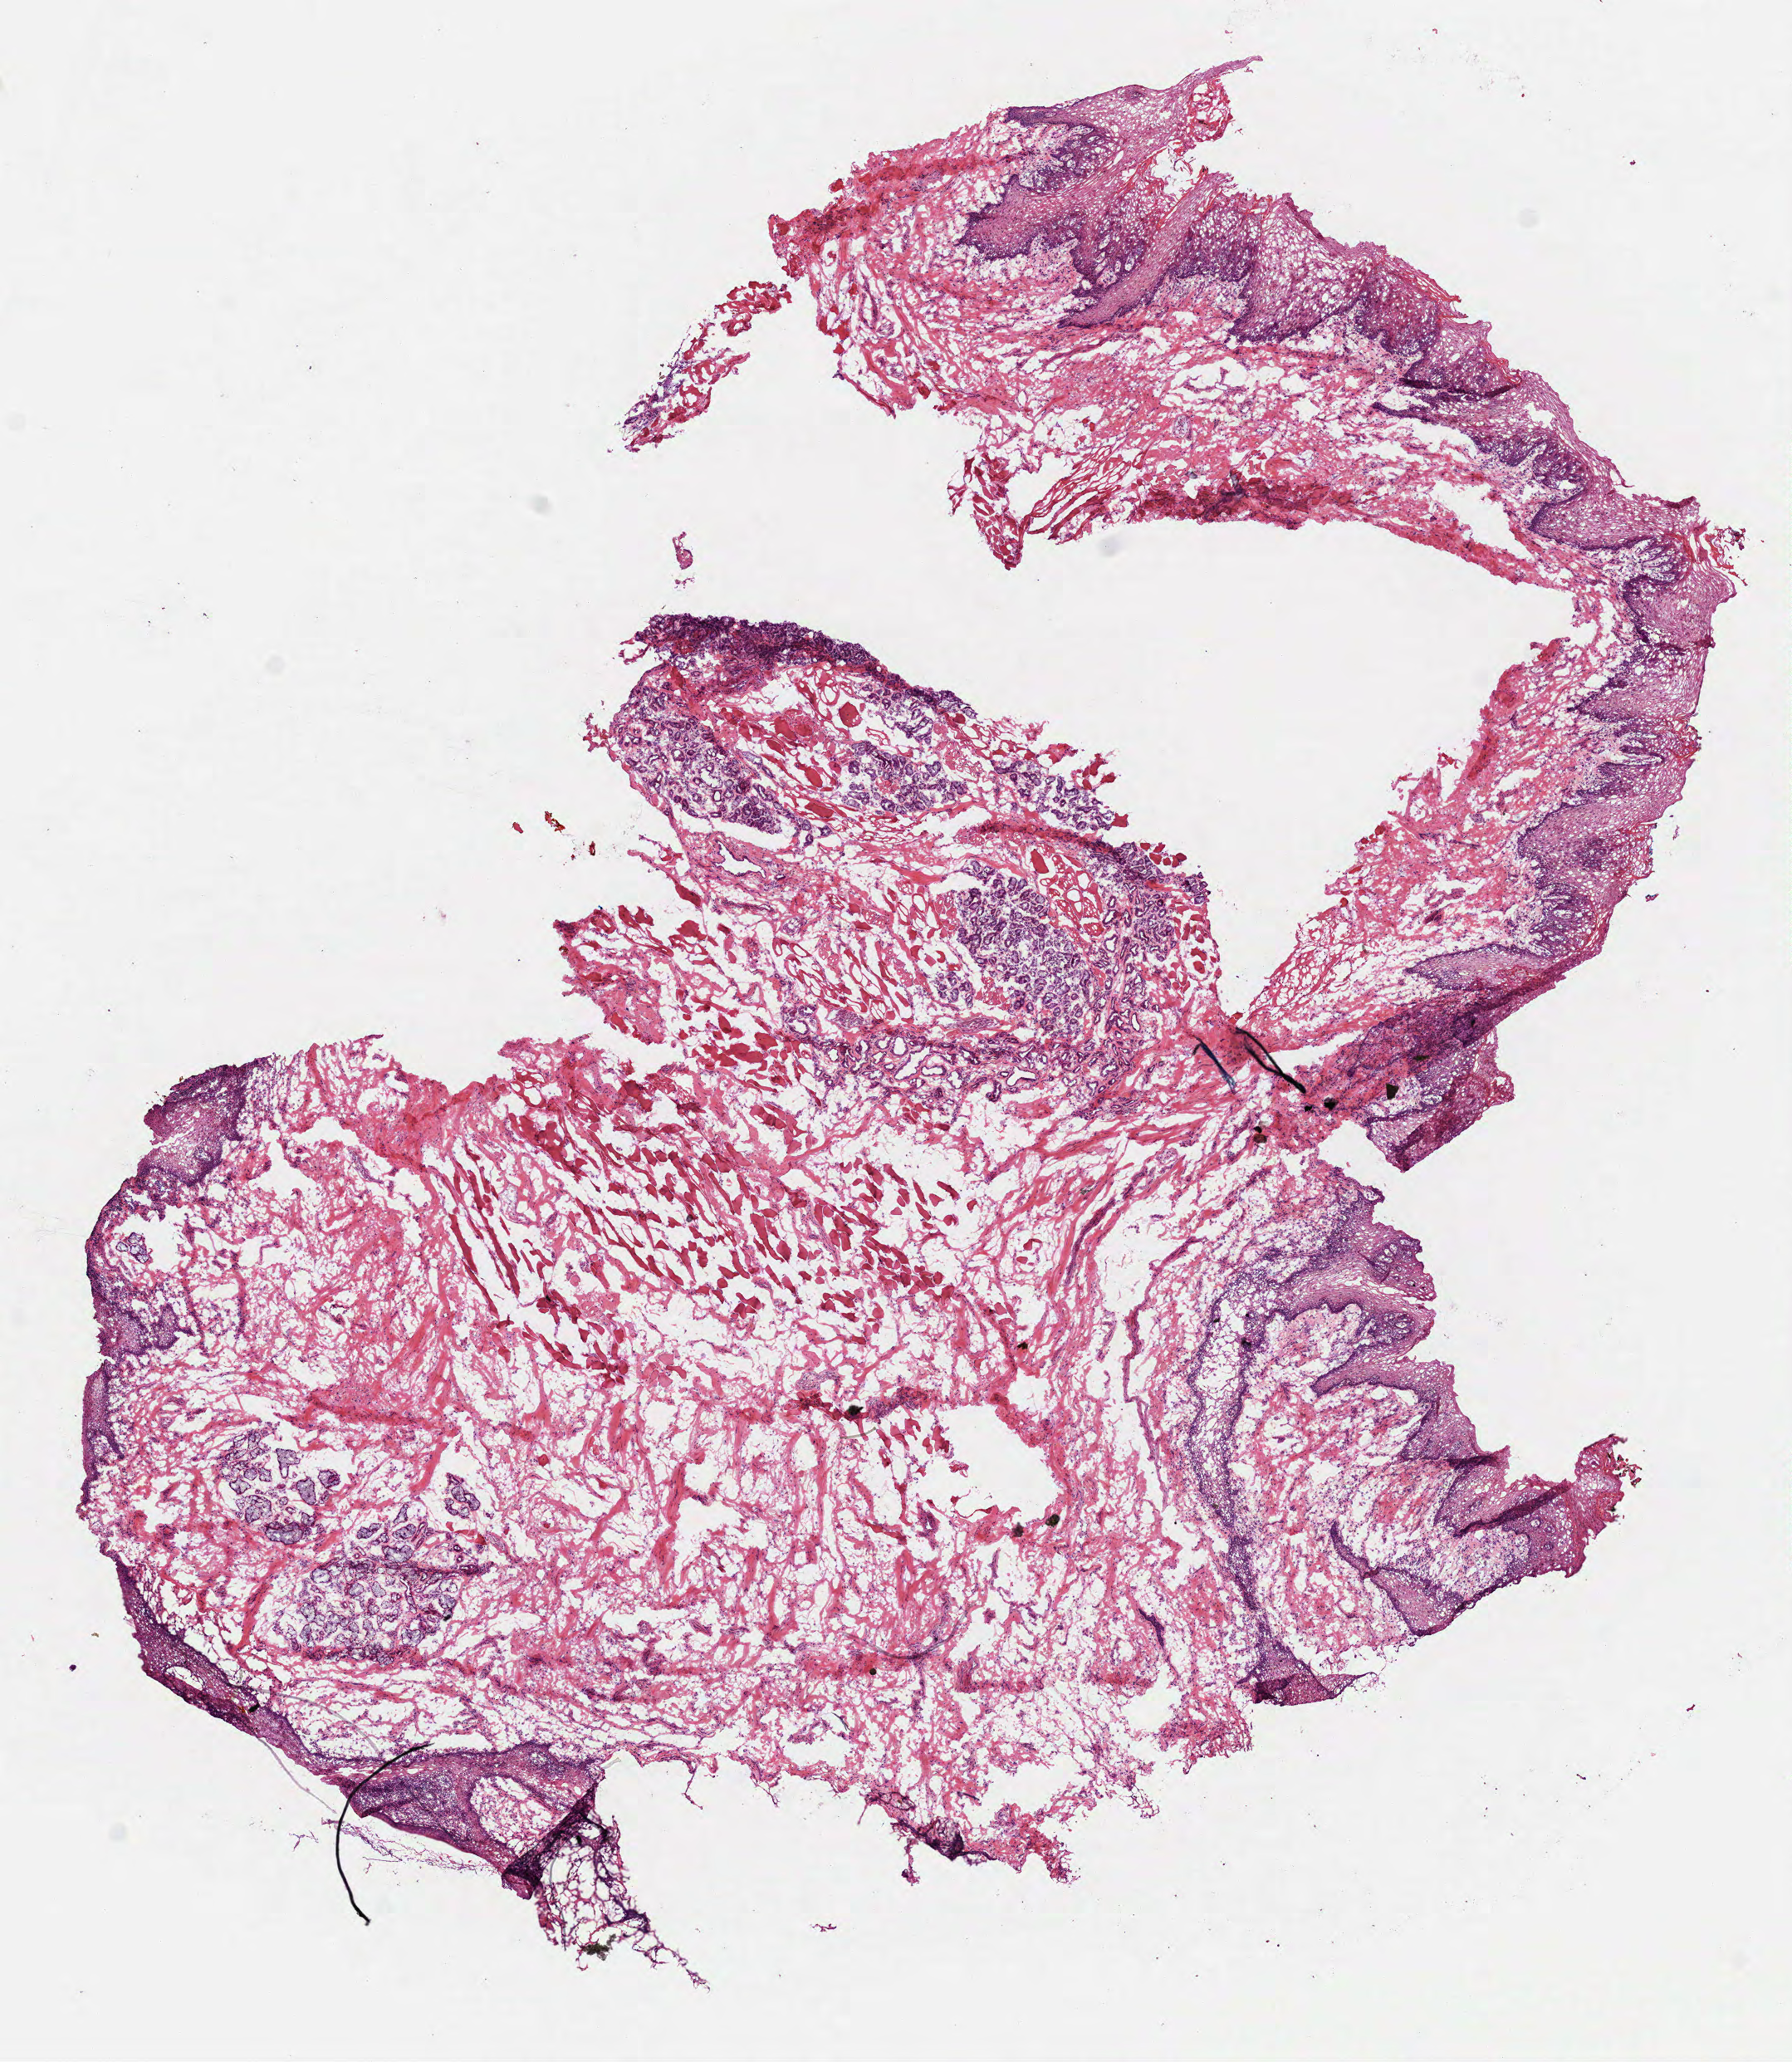
Digitized H&E-stained tissue section (whole slide) — whole scanned area (about 8.7 x 10.0 mm, acquisition: 40x scan) shown as a low-resolution overview. Frozen section. Head and neck, solid tissue normal (non-tumour tissue) sample. Patient: female, age at initial diagnosis 69 years.
- this section: solid tissue normal (non-tumour) sample from the same patient
- patient diagnosis: Squamous cell carcinoma, NOS (tongue, NOS)